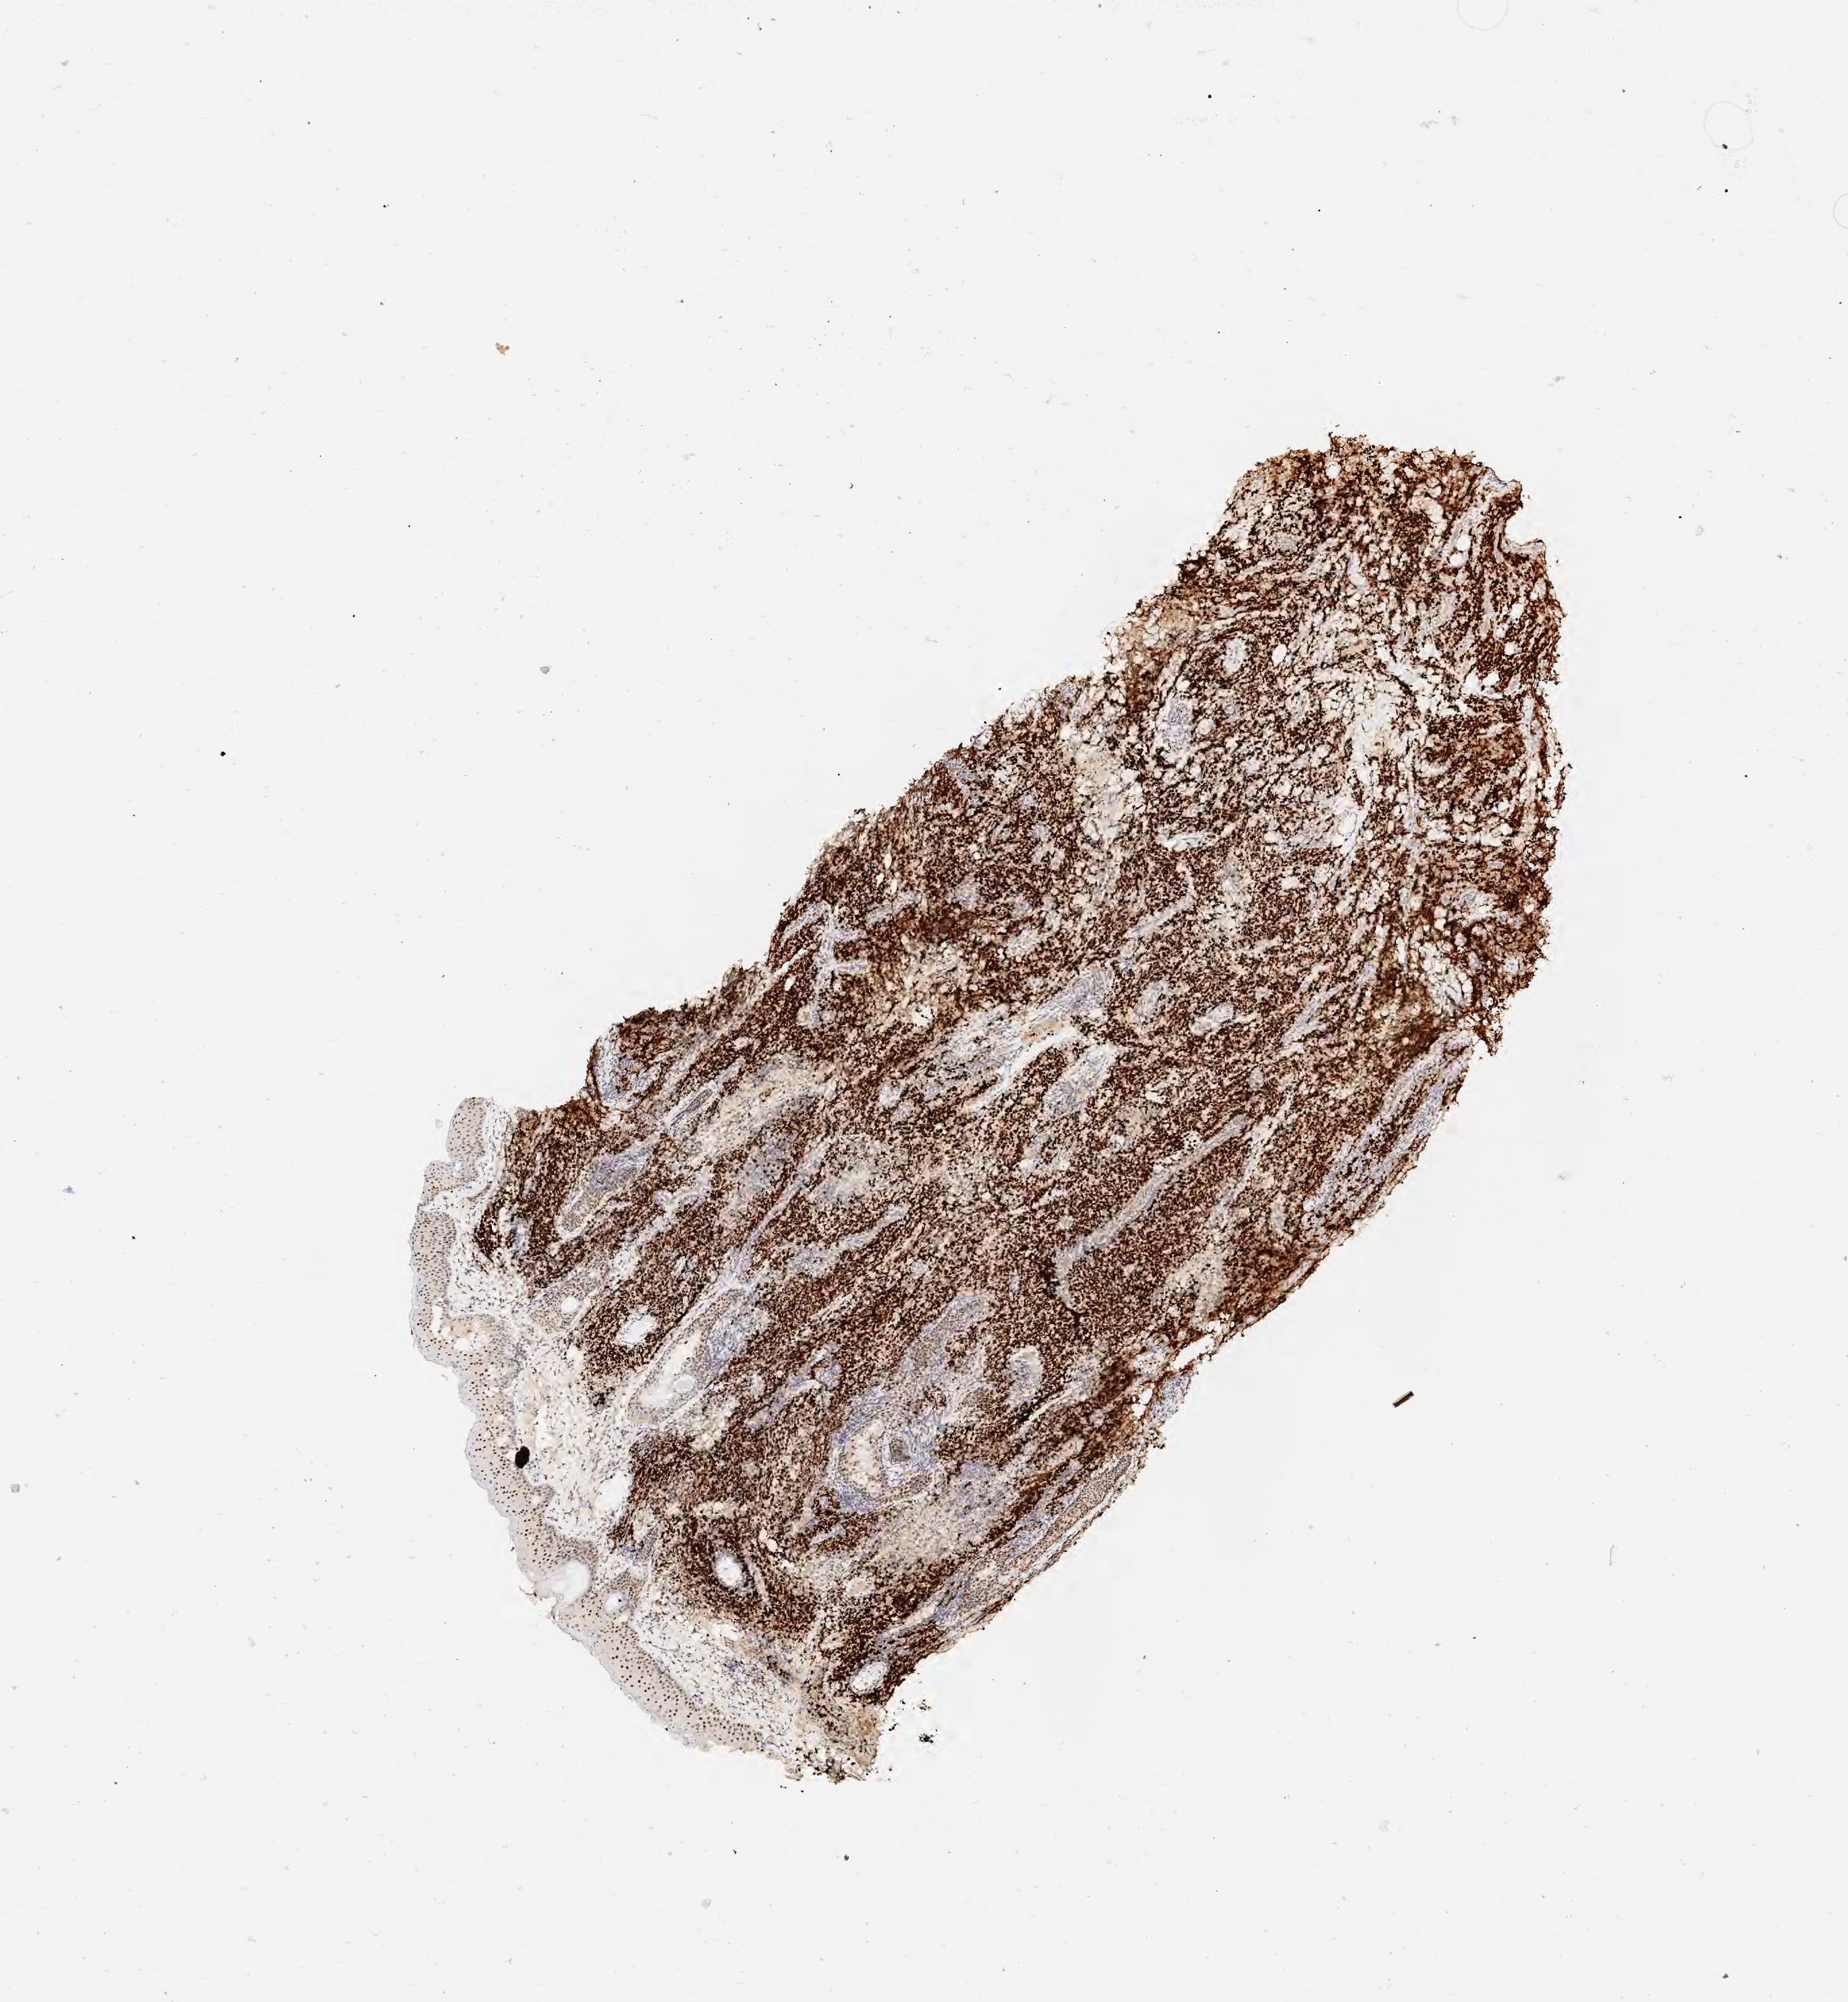
Immunohistochemistry (IHC) whole-slide image stained for BCL6 — whole scanned area (about 5.5 x 6.0 mm) shown as a low-resolution overview, tumor tissue. Patient male; 41 years old.
Diagnosis: Diffuse large B-cell lymphoma, NOS.